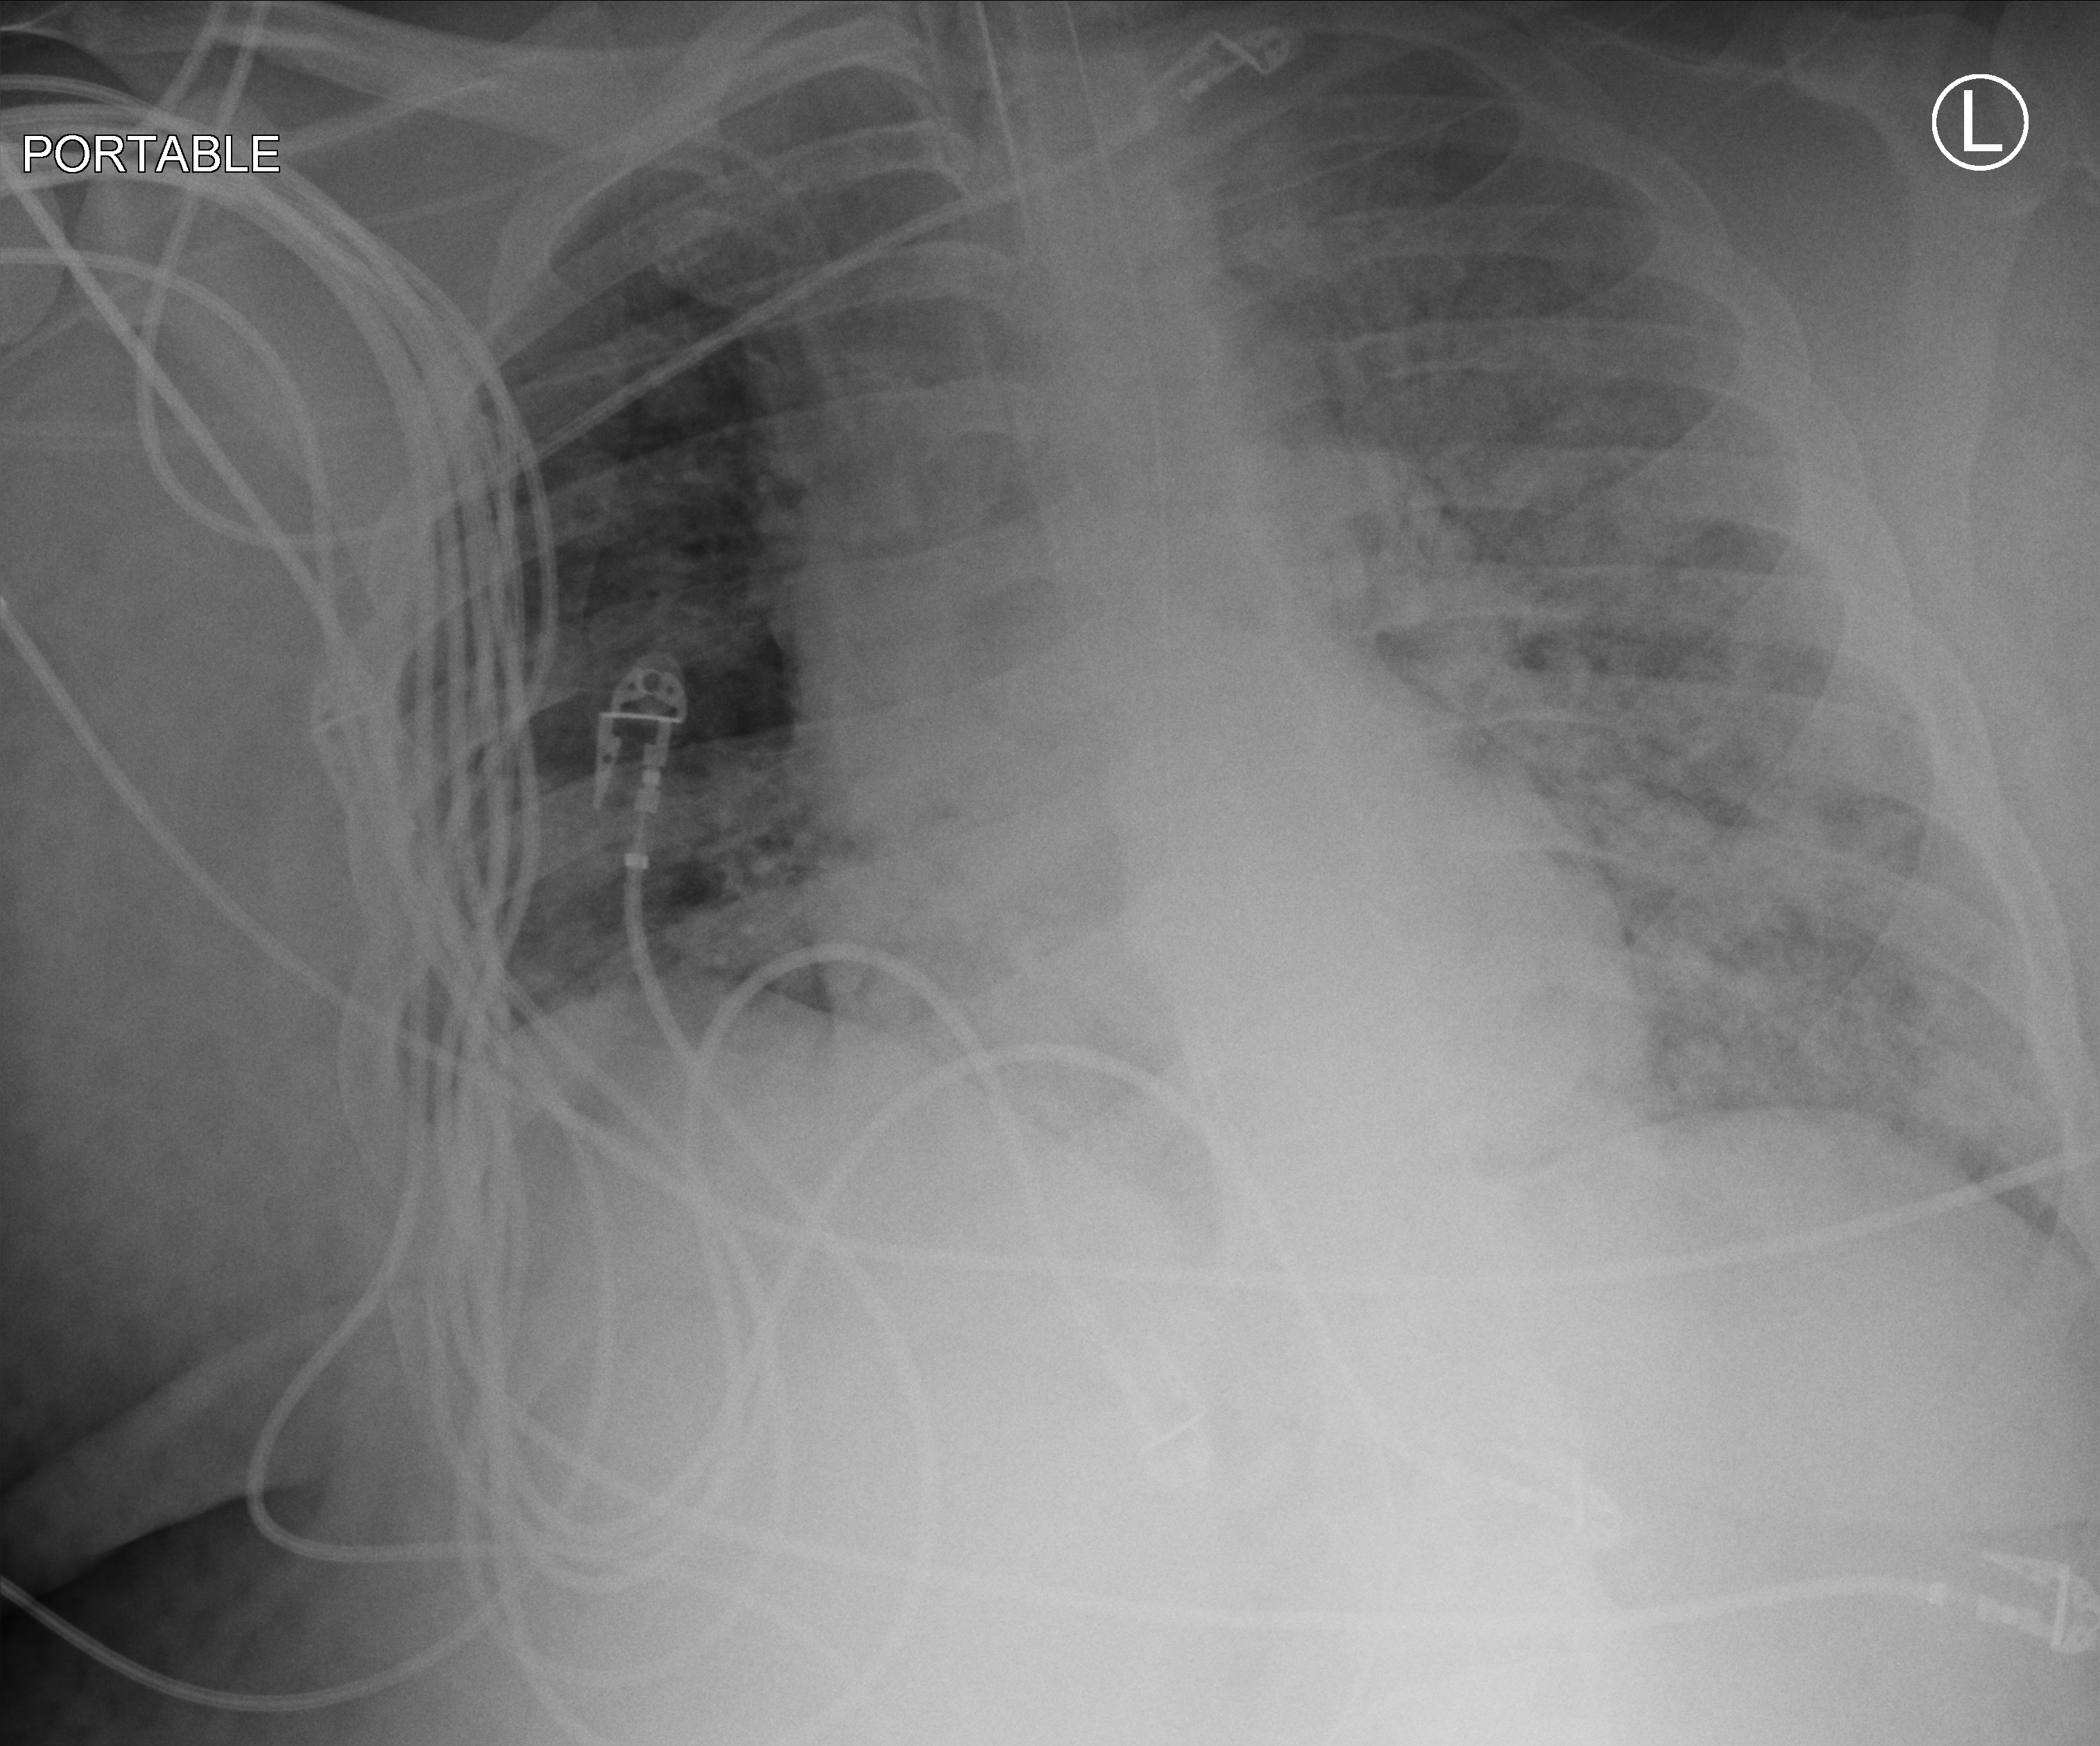
Portable chest radiograph, anteroposterior (AP) projection. Adult patient hospitalised with COVID-19, age 18–59 years.
Admission-level facts for this patient (not findings on this image; timing relative to this image not recorded): mechanically ventilated during this hospital stay: yes.